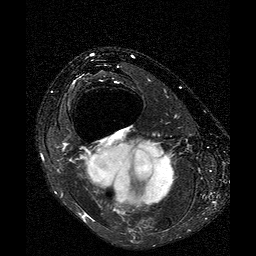
MRI of an extremity soft-tissue mass, one axial slice. Slice 22 of 25 in the series (ordered by position). T2-weighted fat-saturated. 256 × 256 image matrix. Female patient. From the clinical record (not read from this slice): histological type: liposarcoma; site of the primary tumour: right thigh.
Outlined on this slice (outlined manually by an expert reader):
- gross tumour volume (mass): bounding box (x1, y1, x2, y2) in pixels: (83, 138, 174, 215)